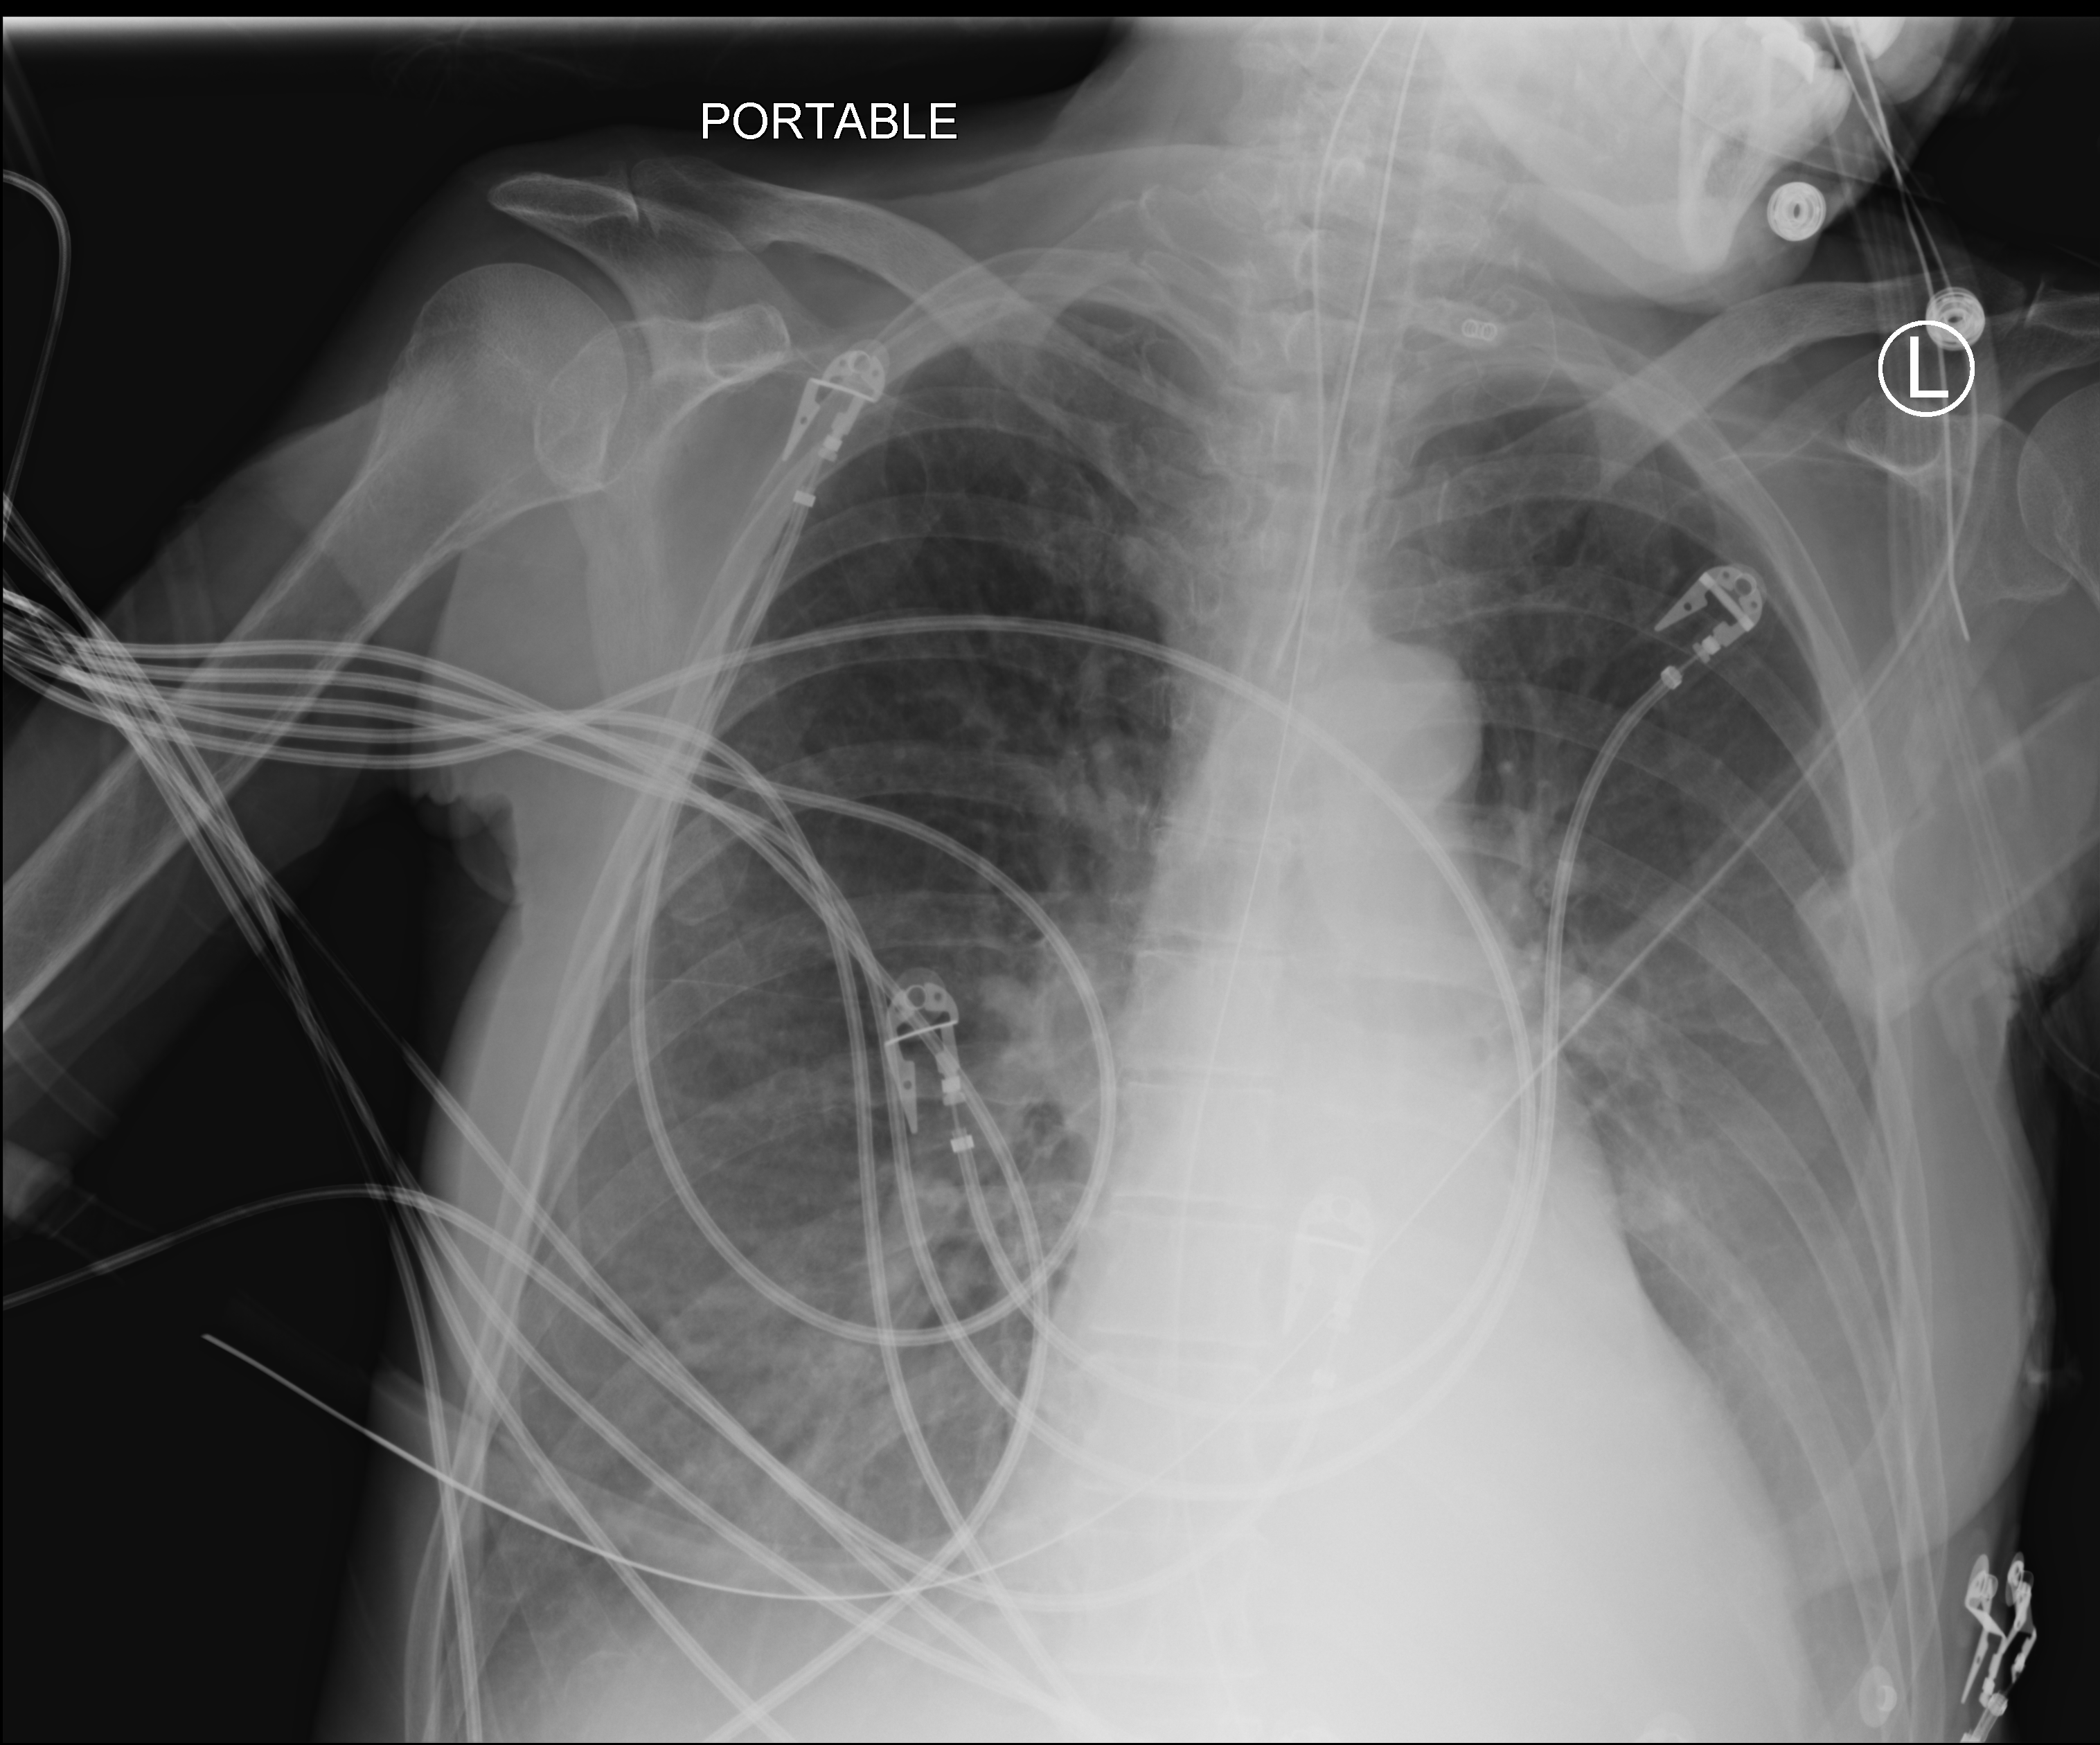
Portable chest radiograph, anteroposterior (AP) projection. Patient hospitalised with COVID-19; female, aged 60–74 years.
Admission-level facts for this patient (not findings on this image; timing relative to this image not recorded): admitted to intensive care during this hospital stay: yes.